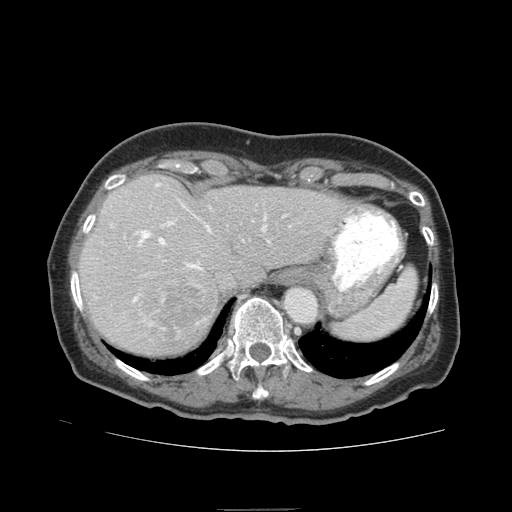
Contrast-enhanced abdominal CT (liver protocol), one axial slice. Slice 63 of 95 in the series (ordered by position). Reconstruction kernel STANDARD. 140 kVp. Soft-tissue window (W 400 / L 40 HU). 2.5 mm slice thickness. 512 × 512 image matrix. Case-level facts recorded for this patient, not image findings: diagnosis: hepatocellular carcinoma (patient treated with transarterial chemoembolisation; whether this scan precedes or follows treatment is not stated here); TNM stage (as recorded): Stage-IVA; Child-Pugh class: B; tumour differentiation: moderately differentiated.
Outlined on this slice (semi-automatic segmentation, software-assisted and operator-edited):
- liver parenchyma outside the tumour (the mass and vessels are separate outlines, so this box may not span the whole liver): bounding box [x1, y1, x2, y2] px = [78, 174, 346, 356]
- mass: [139, 279, 210, 345]
- liver vessels: [133, 183, 269, 302]